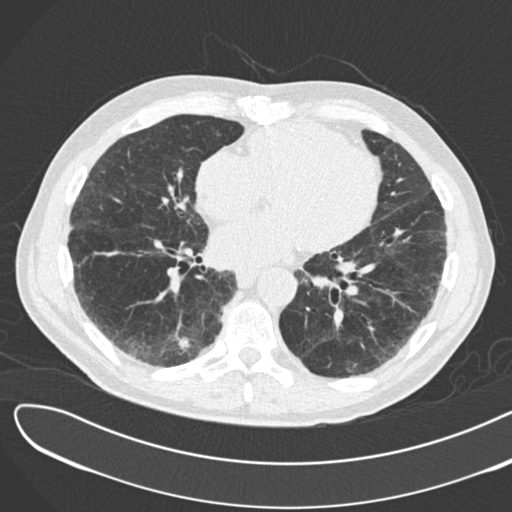
Chest CT (low-dose screening protocol), one axial image; second screening round (one year after baseline); lung window (W 1500 / L -600 HU); 120 kVp. Male participant, aged 72 years at enrolment. Former smoker at enrolment.
- Expert reader's lesion annotation, bounding box [x1, y1, x2, y2] px = [165, 325, 207, 359].
- The screening reader recorded 2 non-calcified nodules or masses ≥4 mm on this exam (right lower lobe, right lower lobe); which of them this box marks is not recorded.
- Official screen result: positive, change unspecified: nodule(s) >= 4 mm or enlarging nodule(s), mass(es), or other non-specific abnormalities suspicious for lung cancer.
- Participant outcome: lung cancer diagnosed 46 days after this screen — squamous cell carcinoma, NOS, right lower lobe, poorly differentiated (G3), stage IB (AJCC 6th edition), 42 mm at pathology.